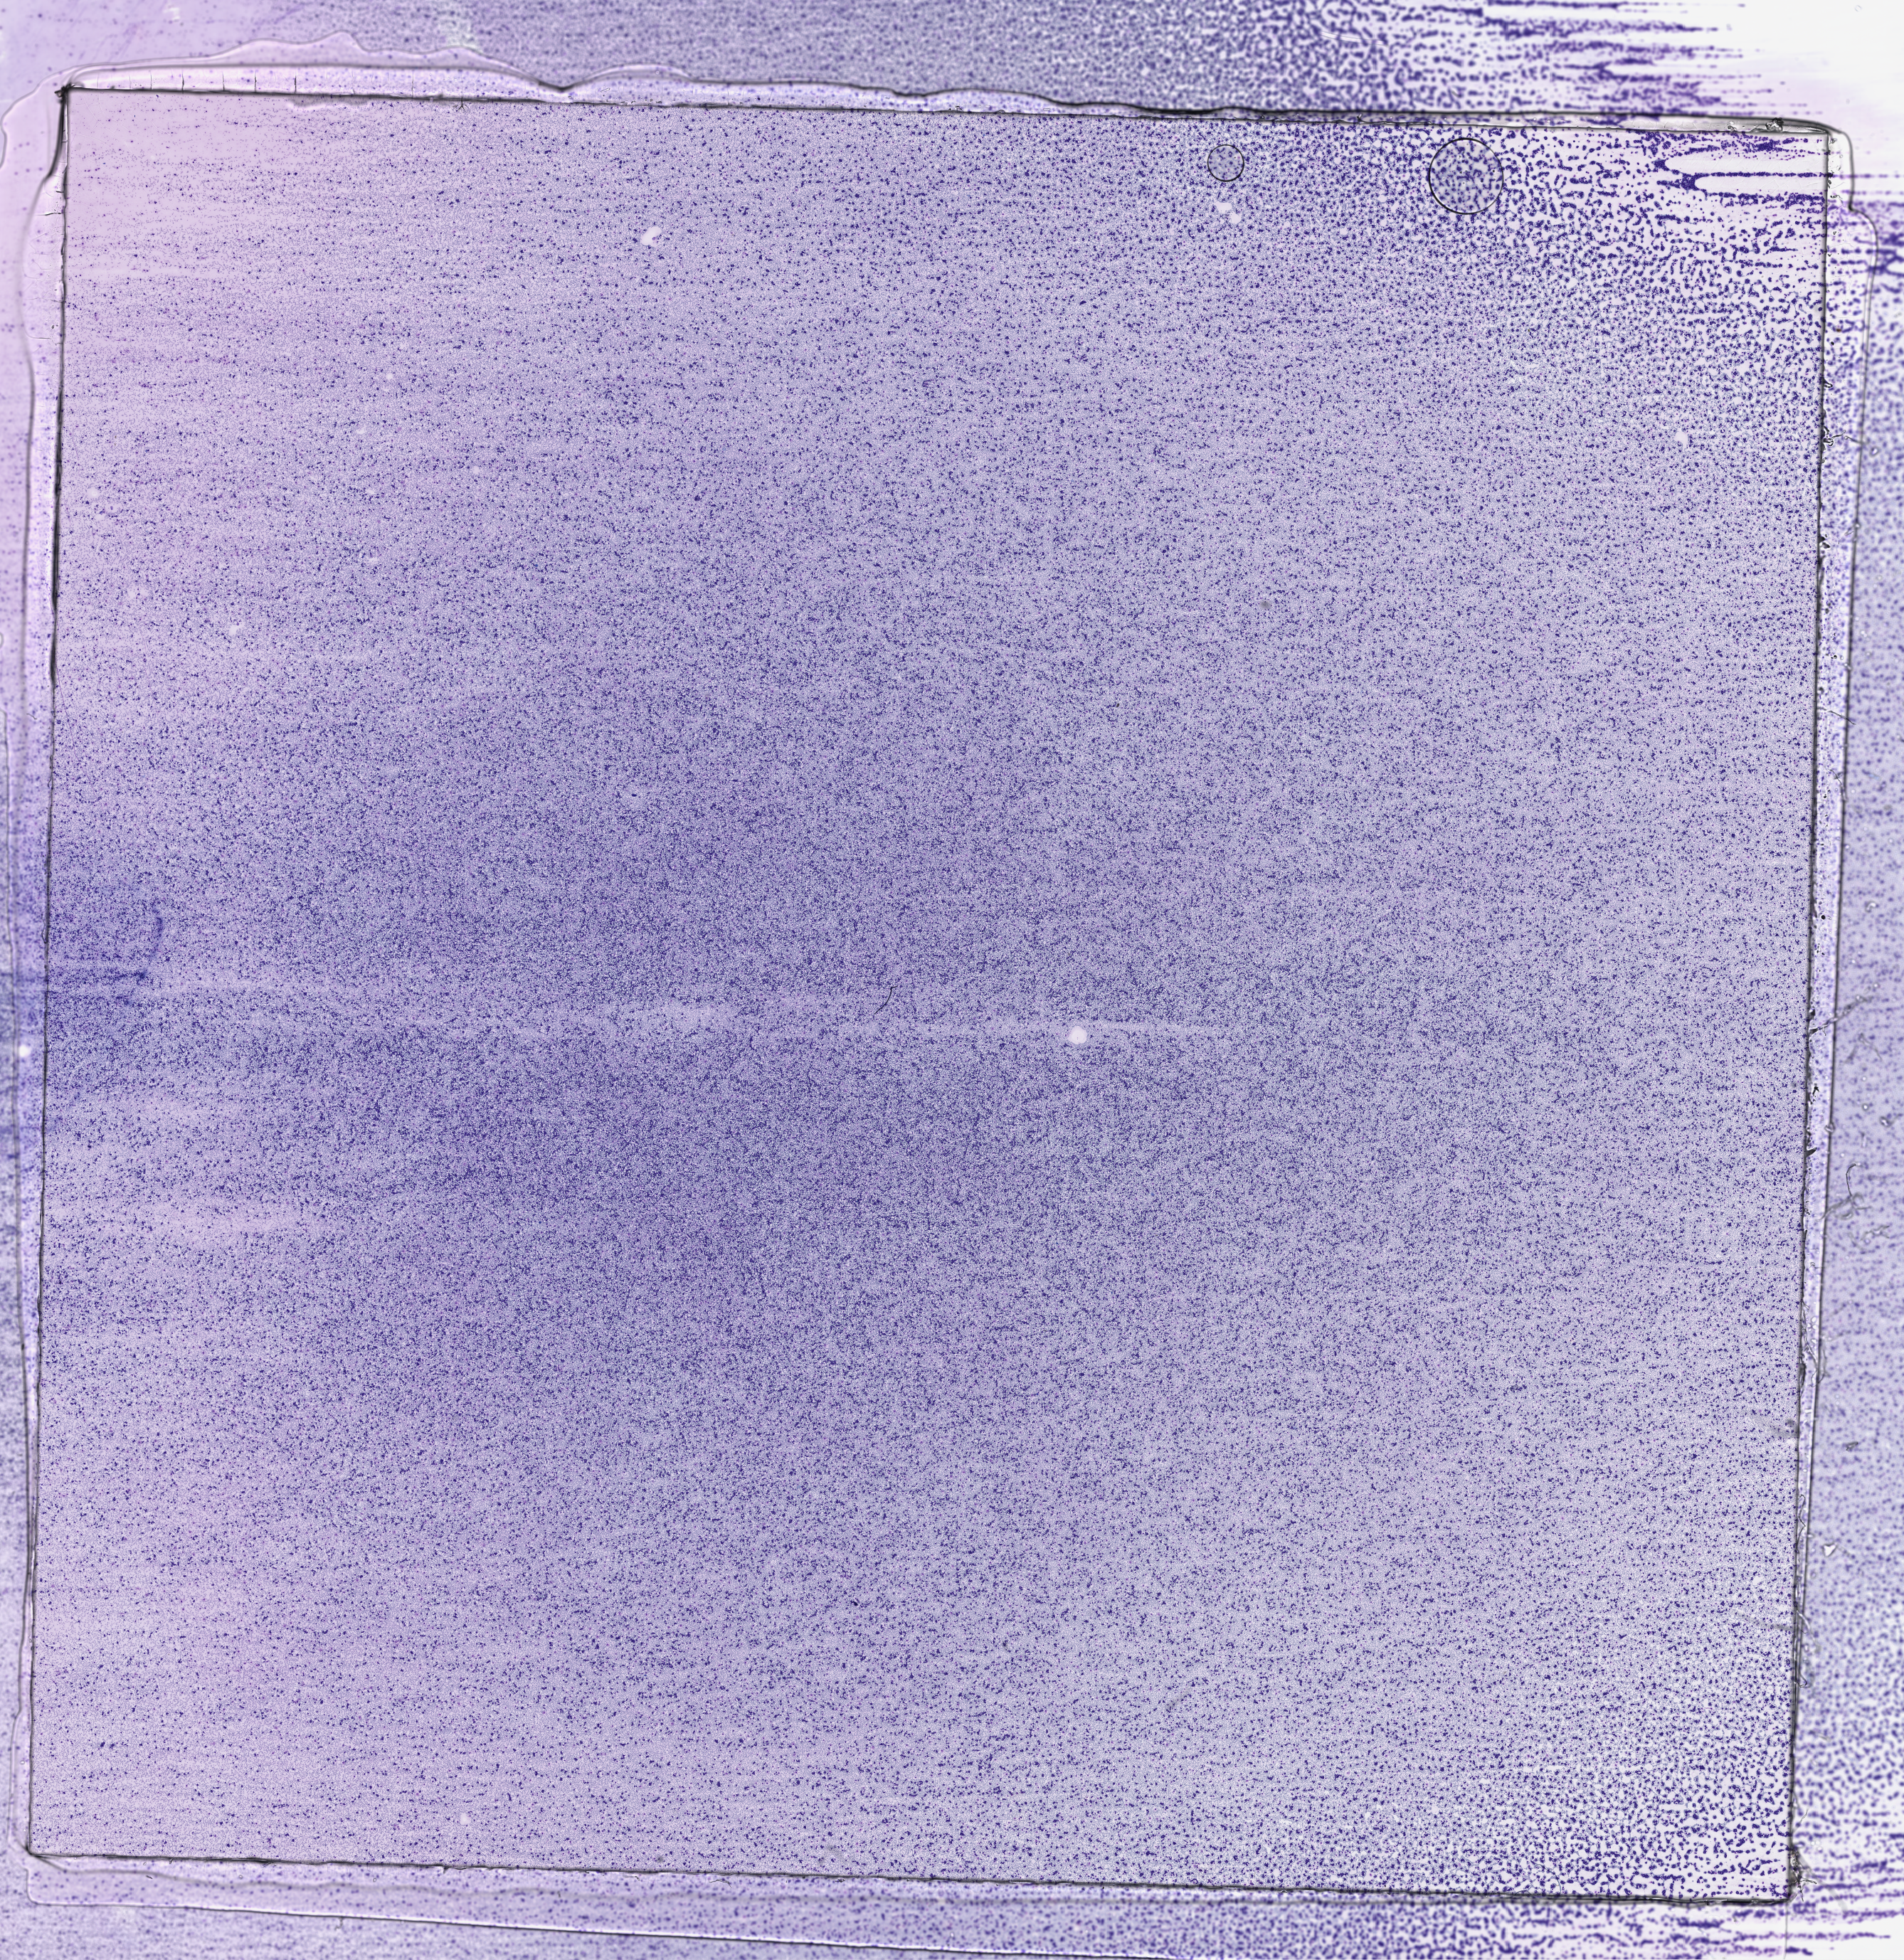
Digitized H&E tissue section (whole slide) — shown as a low-resolution overview of the whole scanned area (about 21.6 x 22.2 mm, from a 40x scan), peripheral blood (leukaemic) sample. Patient: female, age 47 years.
• diagnosis: Acute Myeloid Leukemia
• WHO classification: Acute myelomonocytic leukemia
• FAB classification: M4